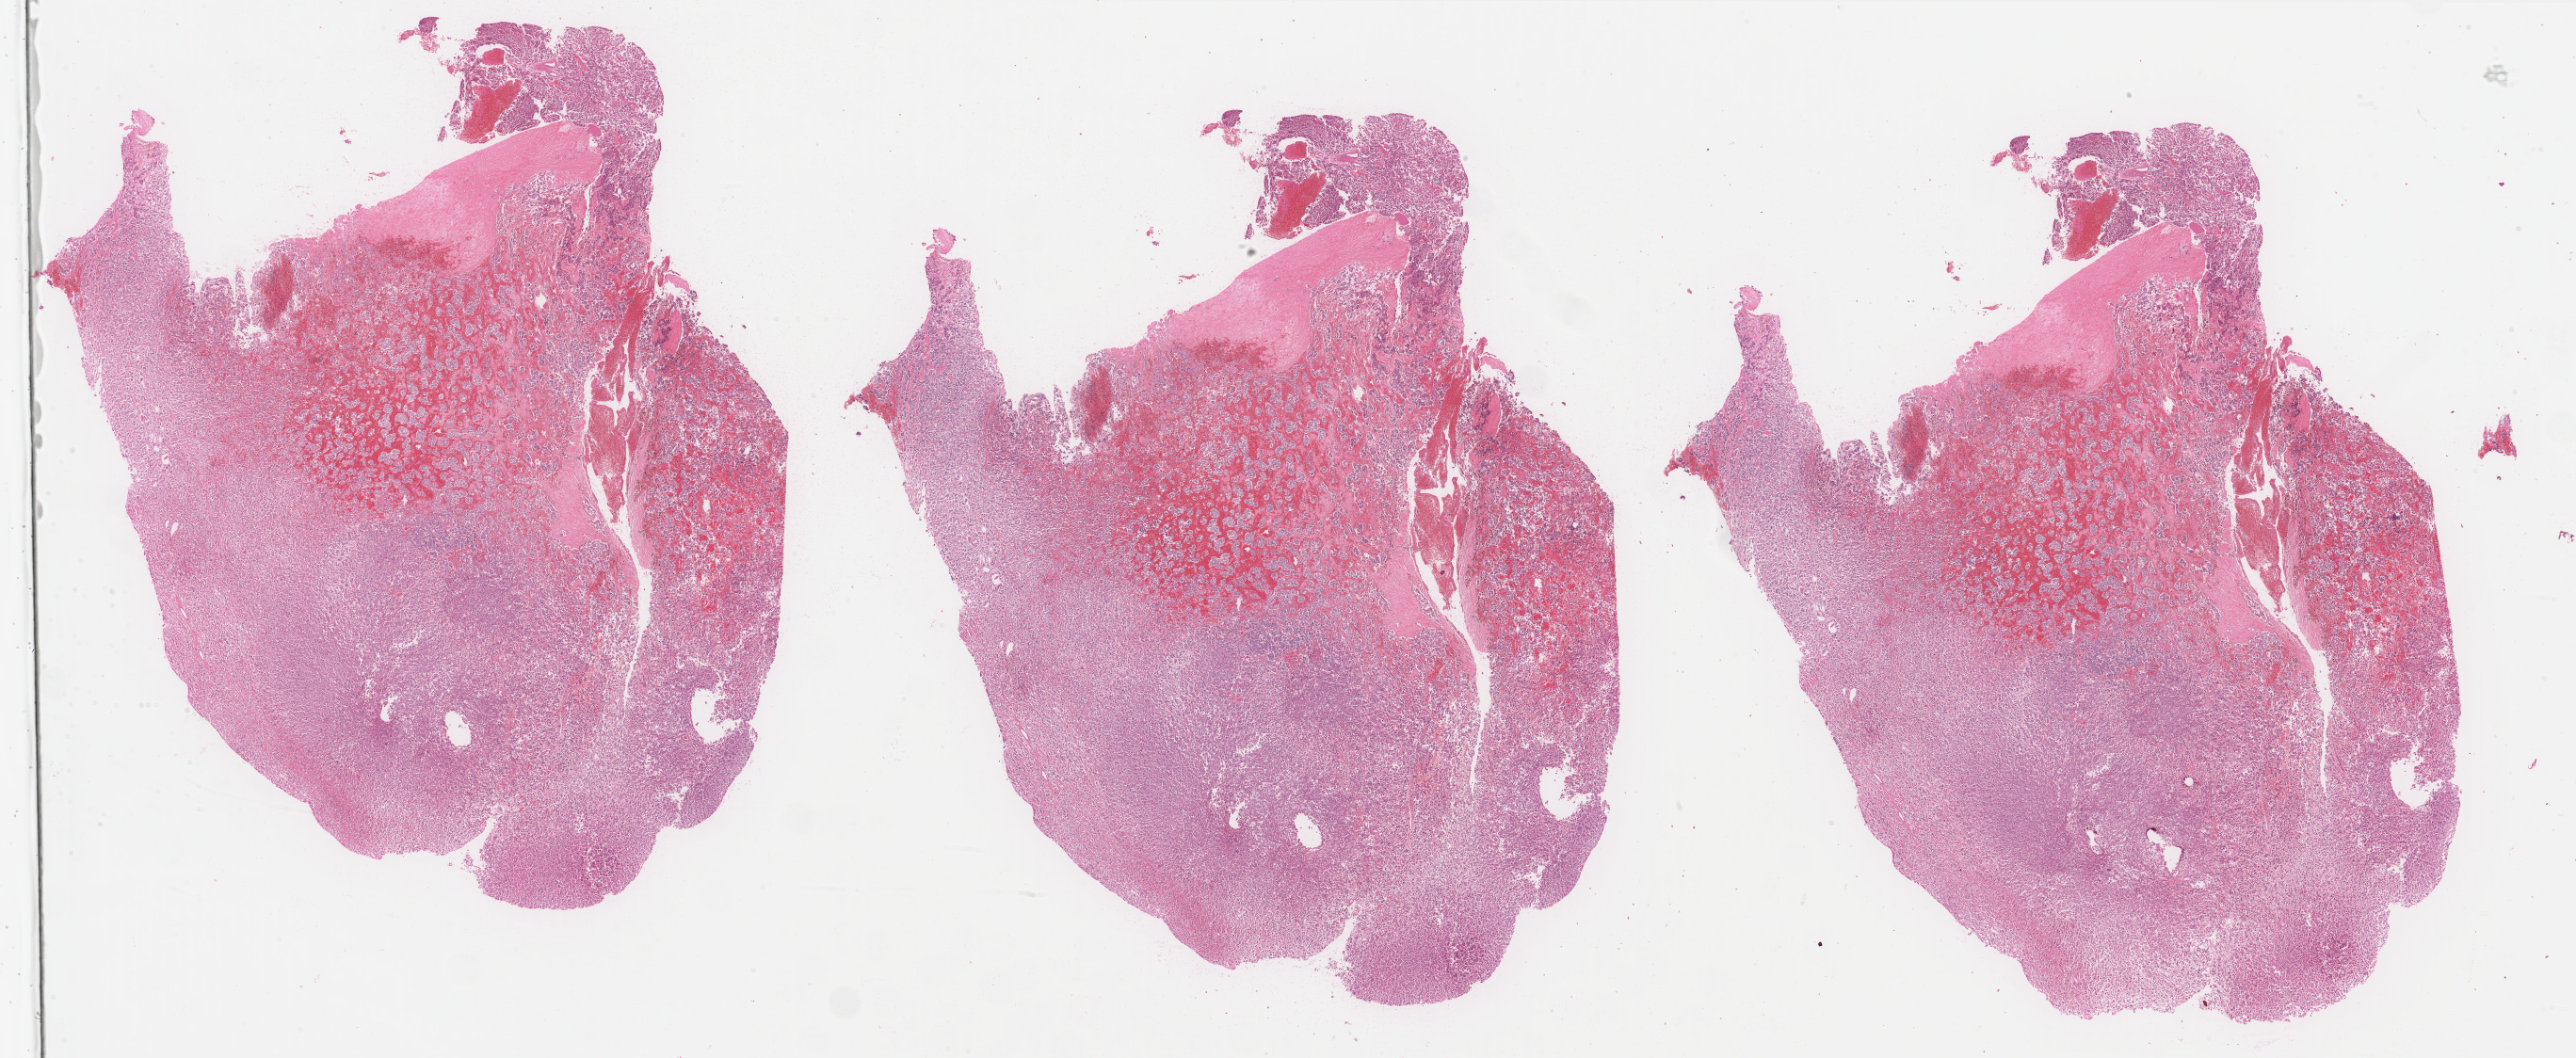
Digitized H&E-stained tissue section (whole slide), low-resolution overview of the scanned area, about 43.3 x 17.8 mm (slide scanned at 40x), formalin-fixed paraffin-embedded (FFPE) diagnostic section, sample: primary tumour, adrenal gland. Female, age 51 years at initial diagnosis.
Pathologic diagnosis: Pheochromocytoma, malignant. Laterality: left.